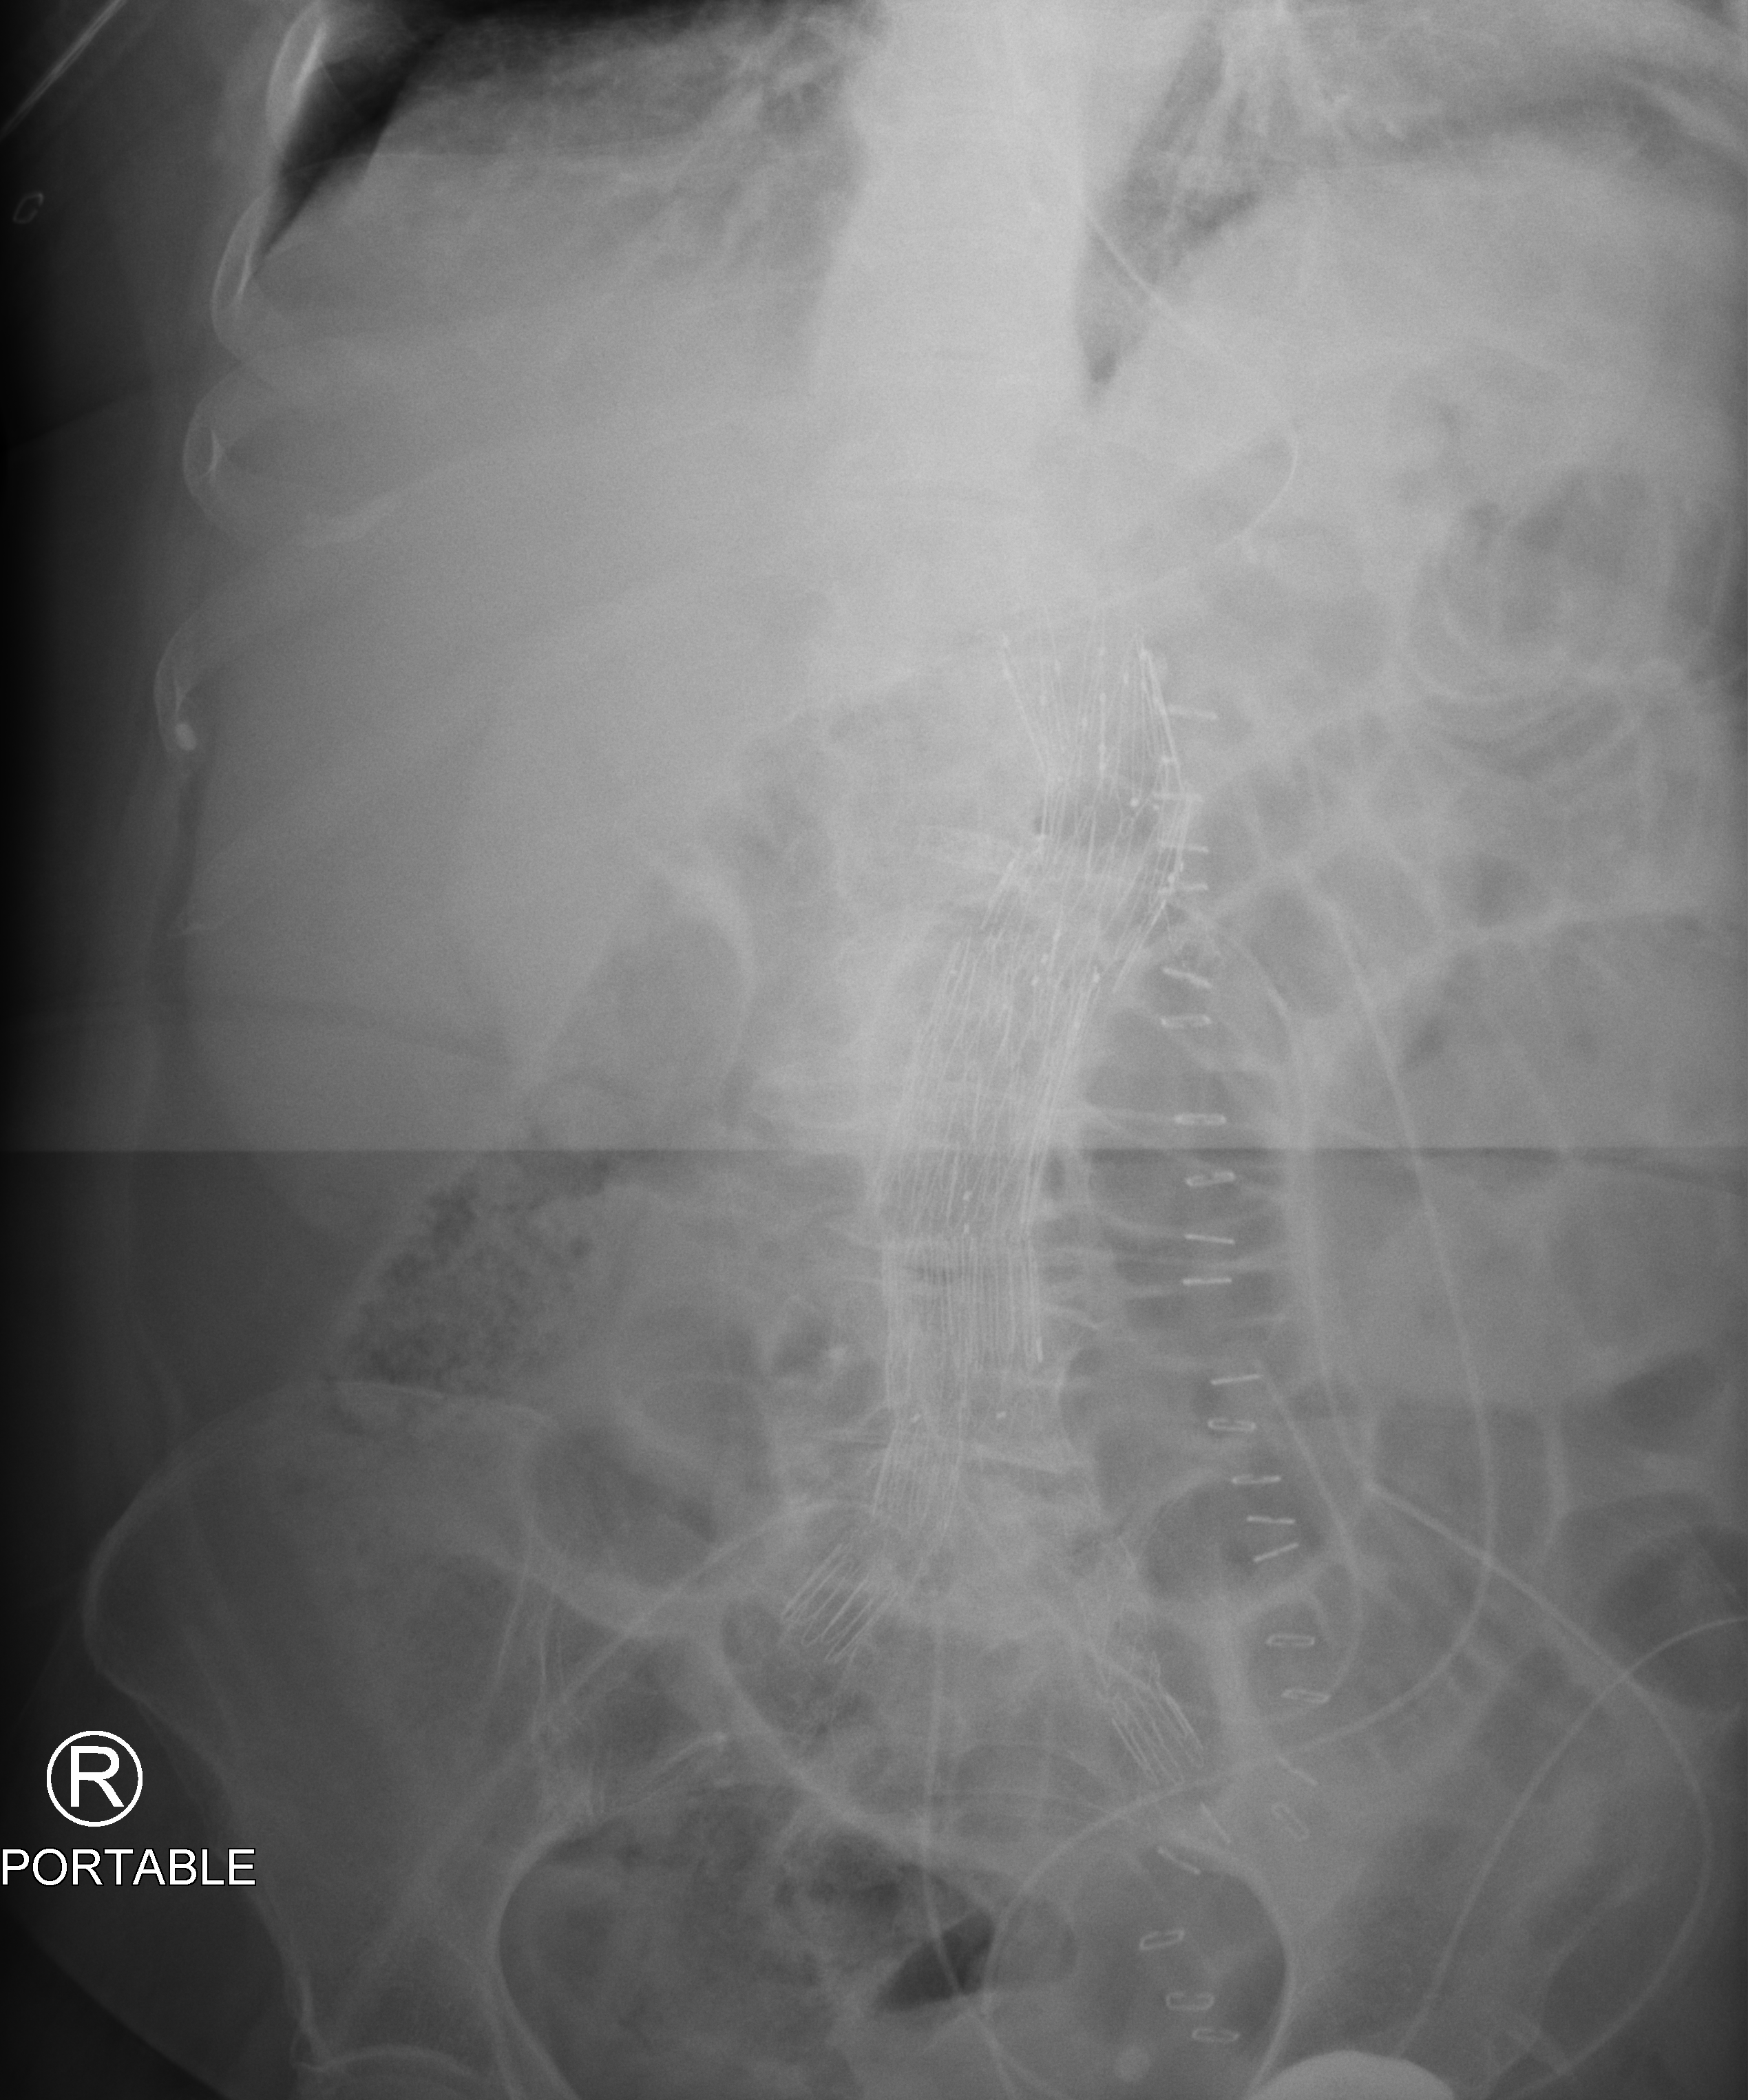
Portable abdomen radiograph, anteroposterior (AP) projection. Female patient hospitalised with COVID-19, age 60–74 years.
Hospital-stay facts (about this admission, not read from this image; timing relative to this image not recorded): mechanically ventilated during this hospital stay: no; length of hospital stay: 9 days; admitted to intensive care during this hospital stay: yes.